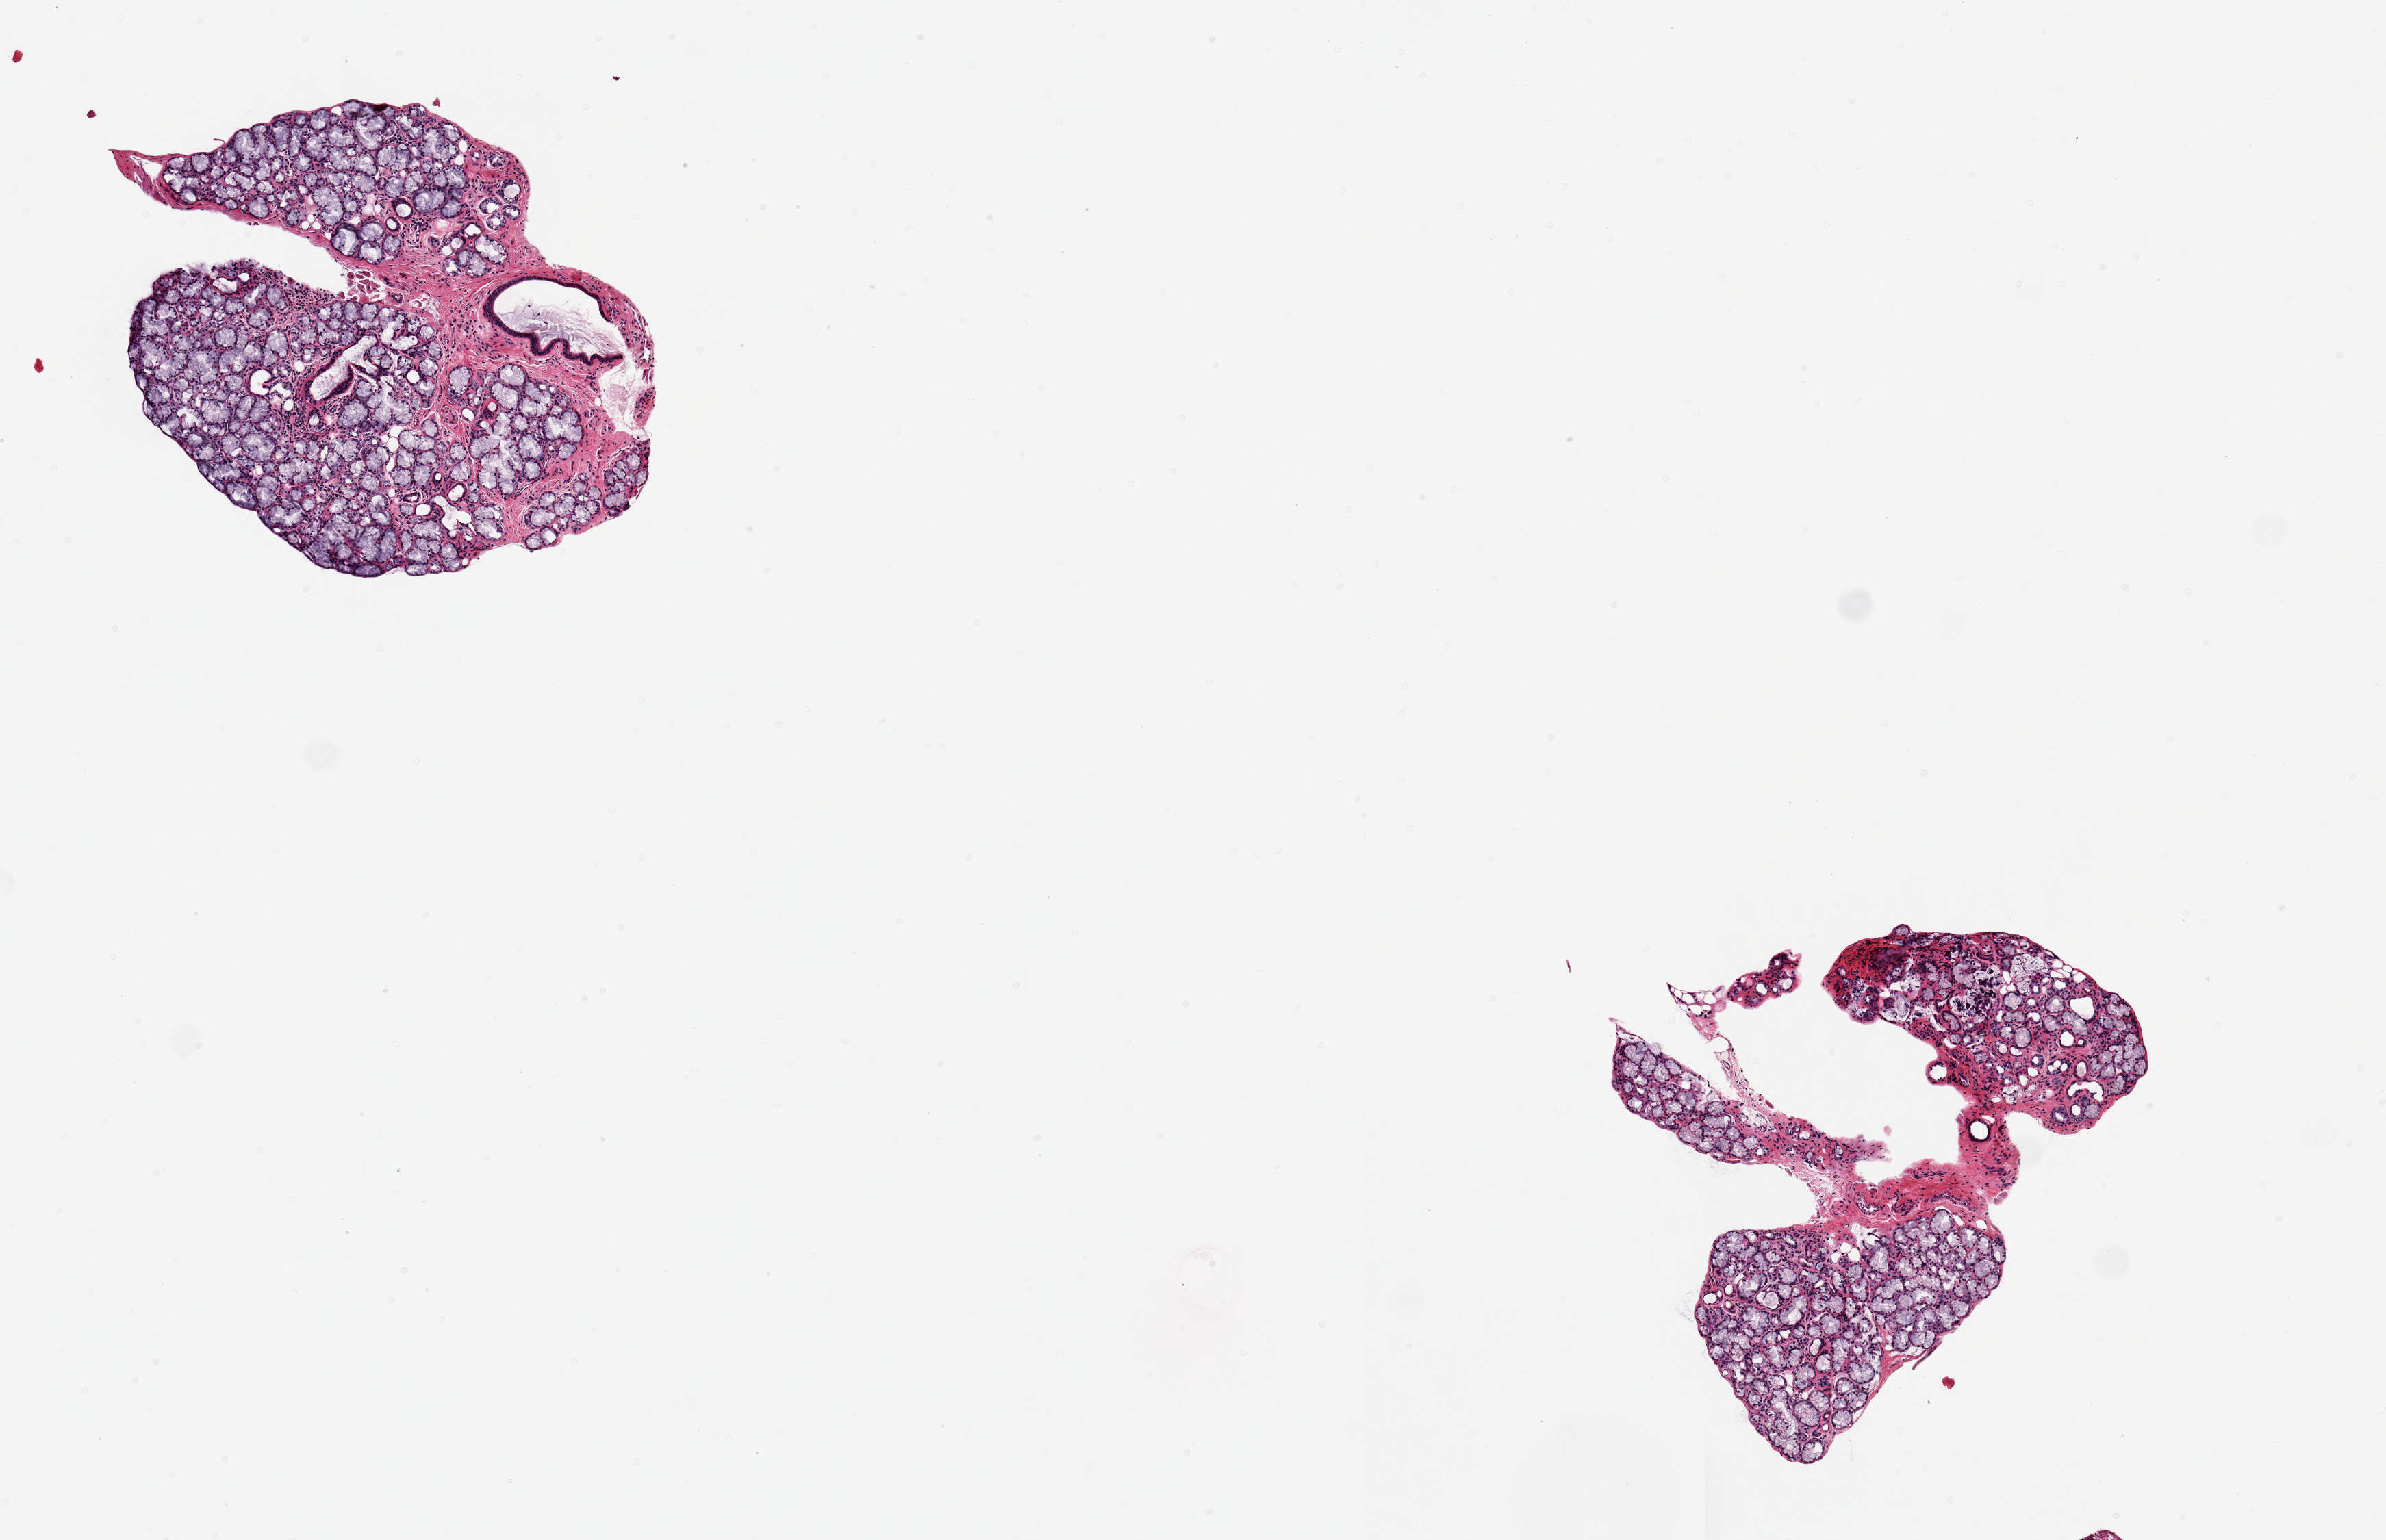
H&E whole-slide image — shown as a low-resolution overview of the whole scanned area (about 6.9 x 4.4 mm, from a 20x scan). PAXgene-fixed, paraffin-embedded tissue. Section of minor salivary gland (target tissue). Donor tissue sample. Female donor.
Reviewer comment on this tissue sample: 2 pieces. 2x1 & 2x1mm; Very well dissected. no extraneous tissue.